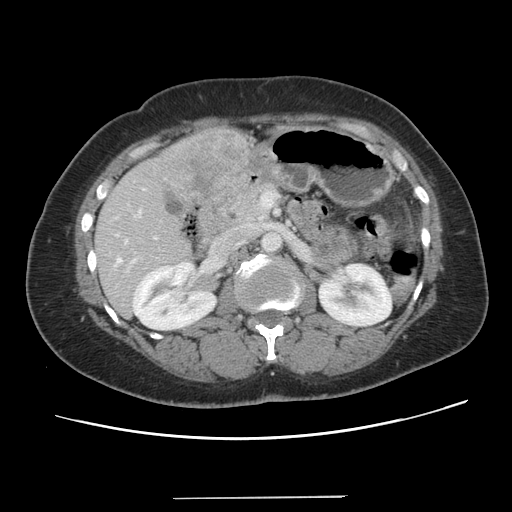
Contrast-enhanced abdominal CT, one axial slice. 120 kVp. Intravenous contrast given. Soft-tissue window (W 400 / L 40 HU). 2.5 mm slice thickness. 512 × 512 image matrix. Female patient, age 53 years. From the clinical record (not read from this slice): diagnosis: colorectal cancer liver metastases, imaged before liver resection.
Outlined on this slice (expert manual segmentation):
- hepatic veins: box from (x=116, y=239) to (x=126, y=263) px
- liver: (x=96, y=128)–(x=248, y=316)
- planned liver remnant (the part of the liver to remain after resection): (x=95, y=215)–(x=190, y=316)
- portal vein (with intrahepatic branches): (x=132, y=214)–(x=140, y=262)
- liver metastasis: (x=167, y=131)–(x=242, y=197)